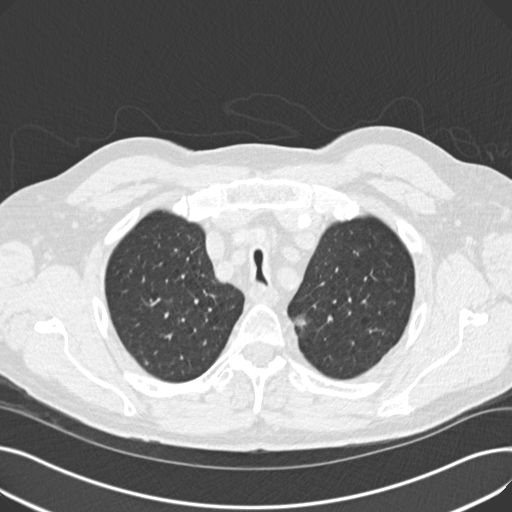
Low-dose screening chest CT, axial slice. Second screening round (one year after baseline). Lung window (W 1500 / L -600 HU). 2 mm slice thickness. 140 kVp. Slice 40 of 187 in the series. Male, age 70 years at enrolment. Current smoker at enrolment.
• Expert reader's lesion annotation, bounding box [x1, y1, x2, y2] px = [279, 302, 318, 343].
• The screening reader recorded 2 non-calcified nodules or masses ≥4 mm on this exam; which of them this box marks is not recorded.
• Official screen result: positive, other.
• Lung cancer was diagnosed 581 days after this screen: mixed cell adenocarcinoma, left upper lobe, poorly differentiated (G3), stage IIB (AJCC 6th edition), 17 mm at pathology.